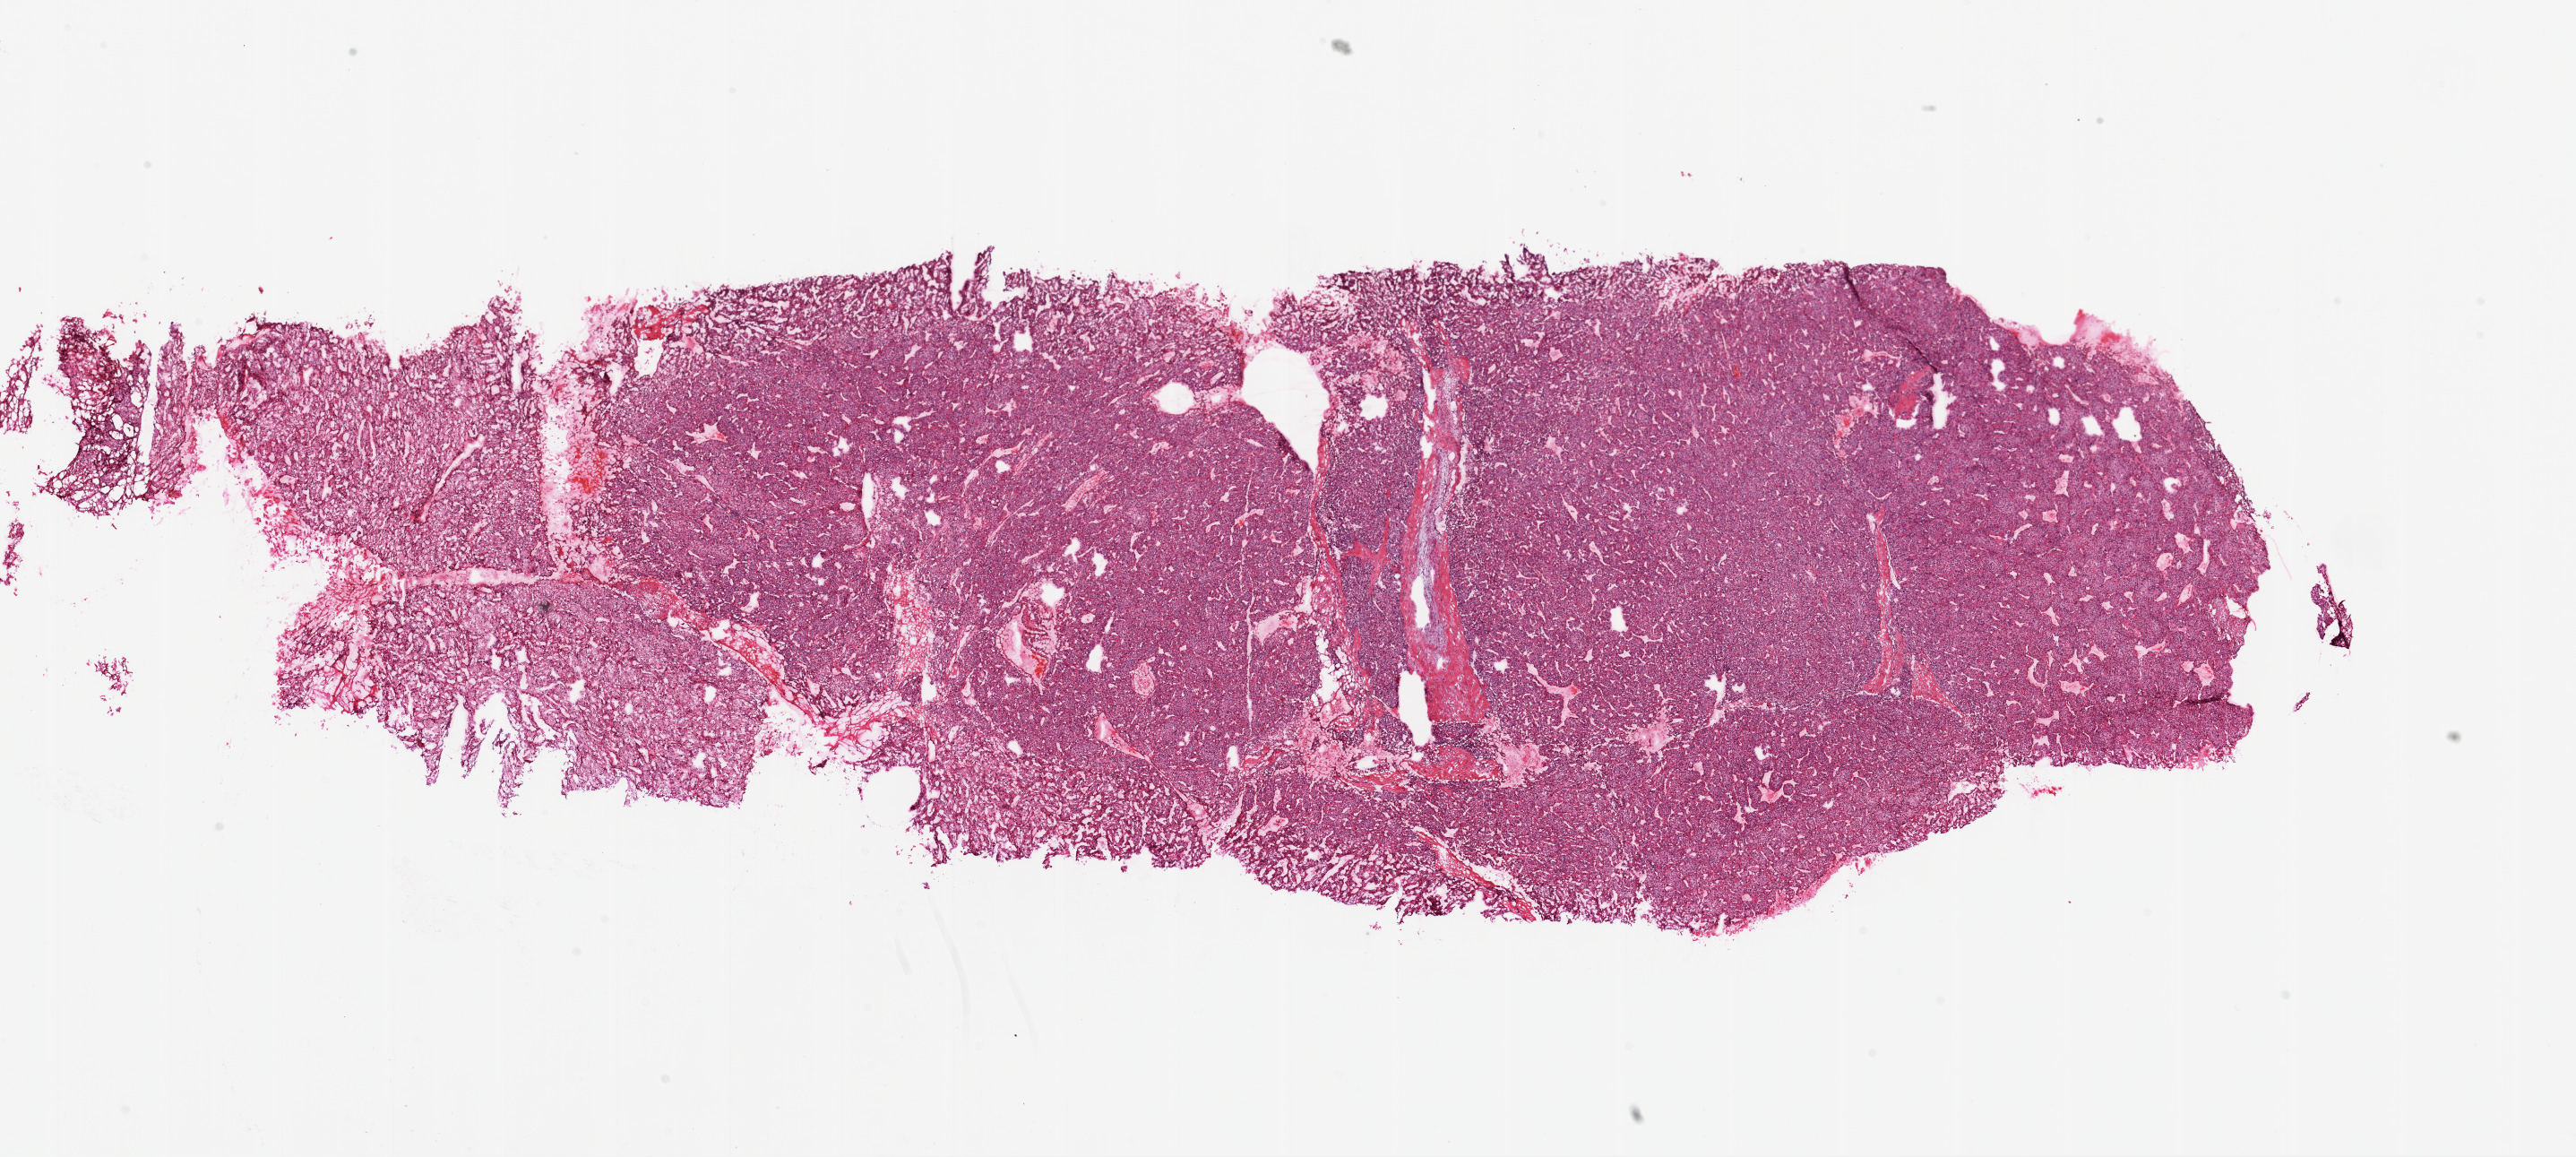
H&E-stained whole-slide image, low-resolution overview of the scanned area, about 23.1 x 10.4 mm (slide scanned at 20x). Frozen section from the top of the tissue portion. Sample: primary tumour, kidney. Patient: male, age at initial diagnosis 61 years. Histologic grade: G3 (poorly differentiated). Composition of this section per pathologist review: tumour cells 90%, tumour nuclei 85%, normal cells 0%, stromal cells 10%, necrosis 0%.
Histologic diagnosis: Clear cell adenocarcinoma, NOS. AJCC pathologic stage: II.